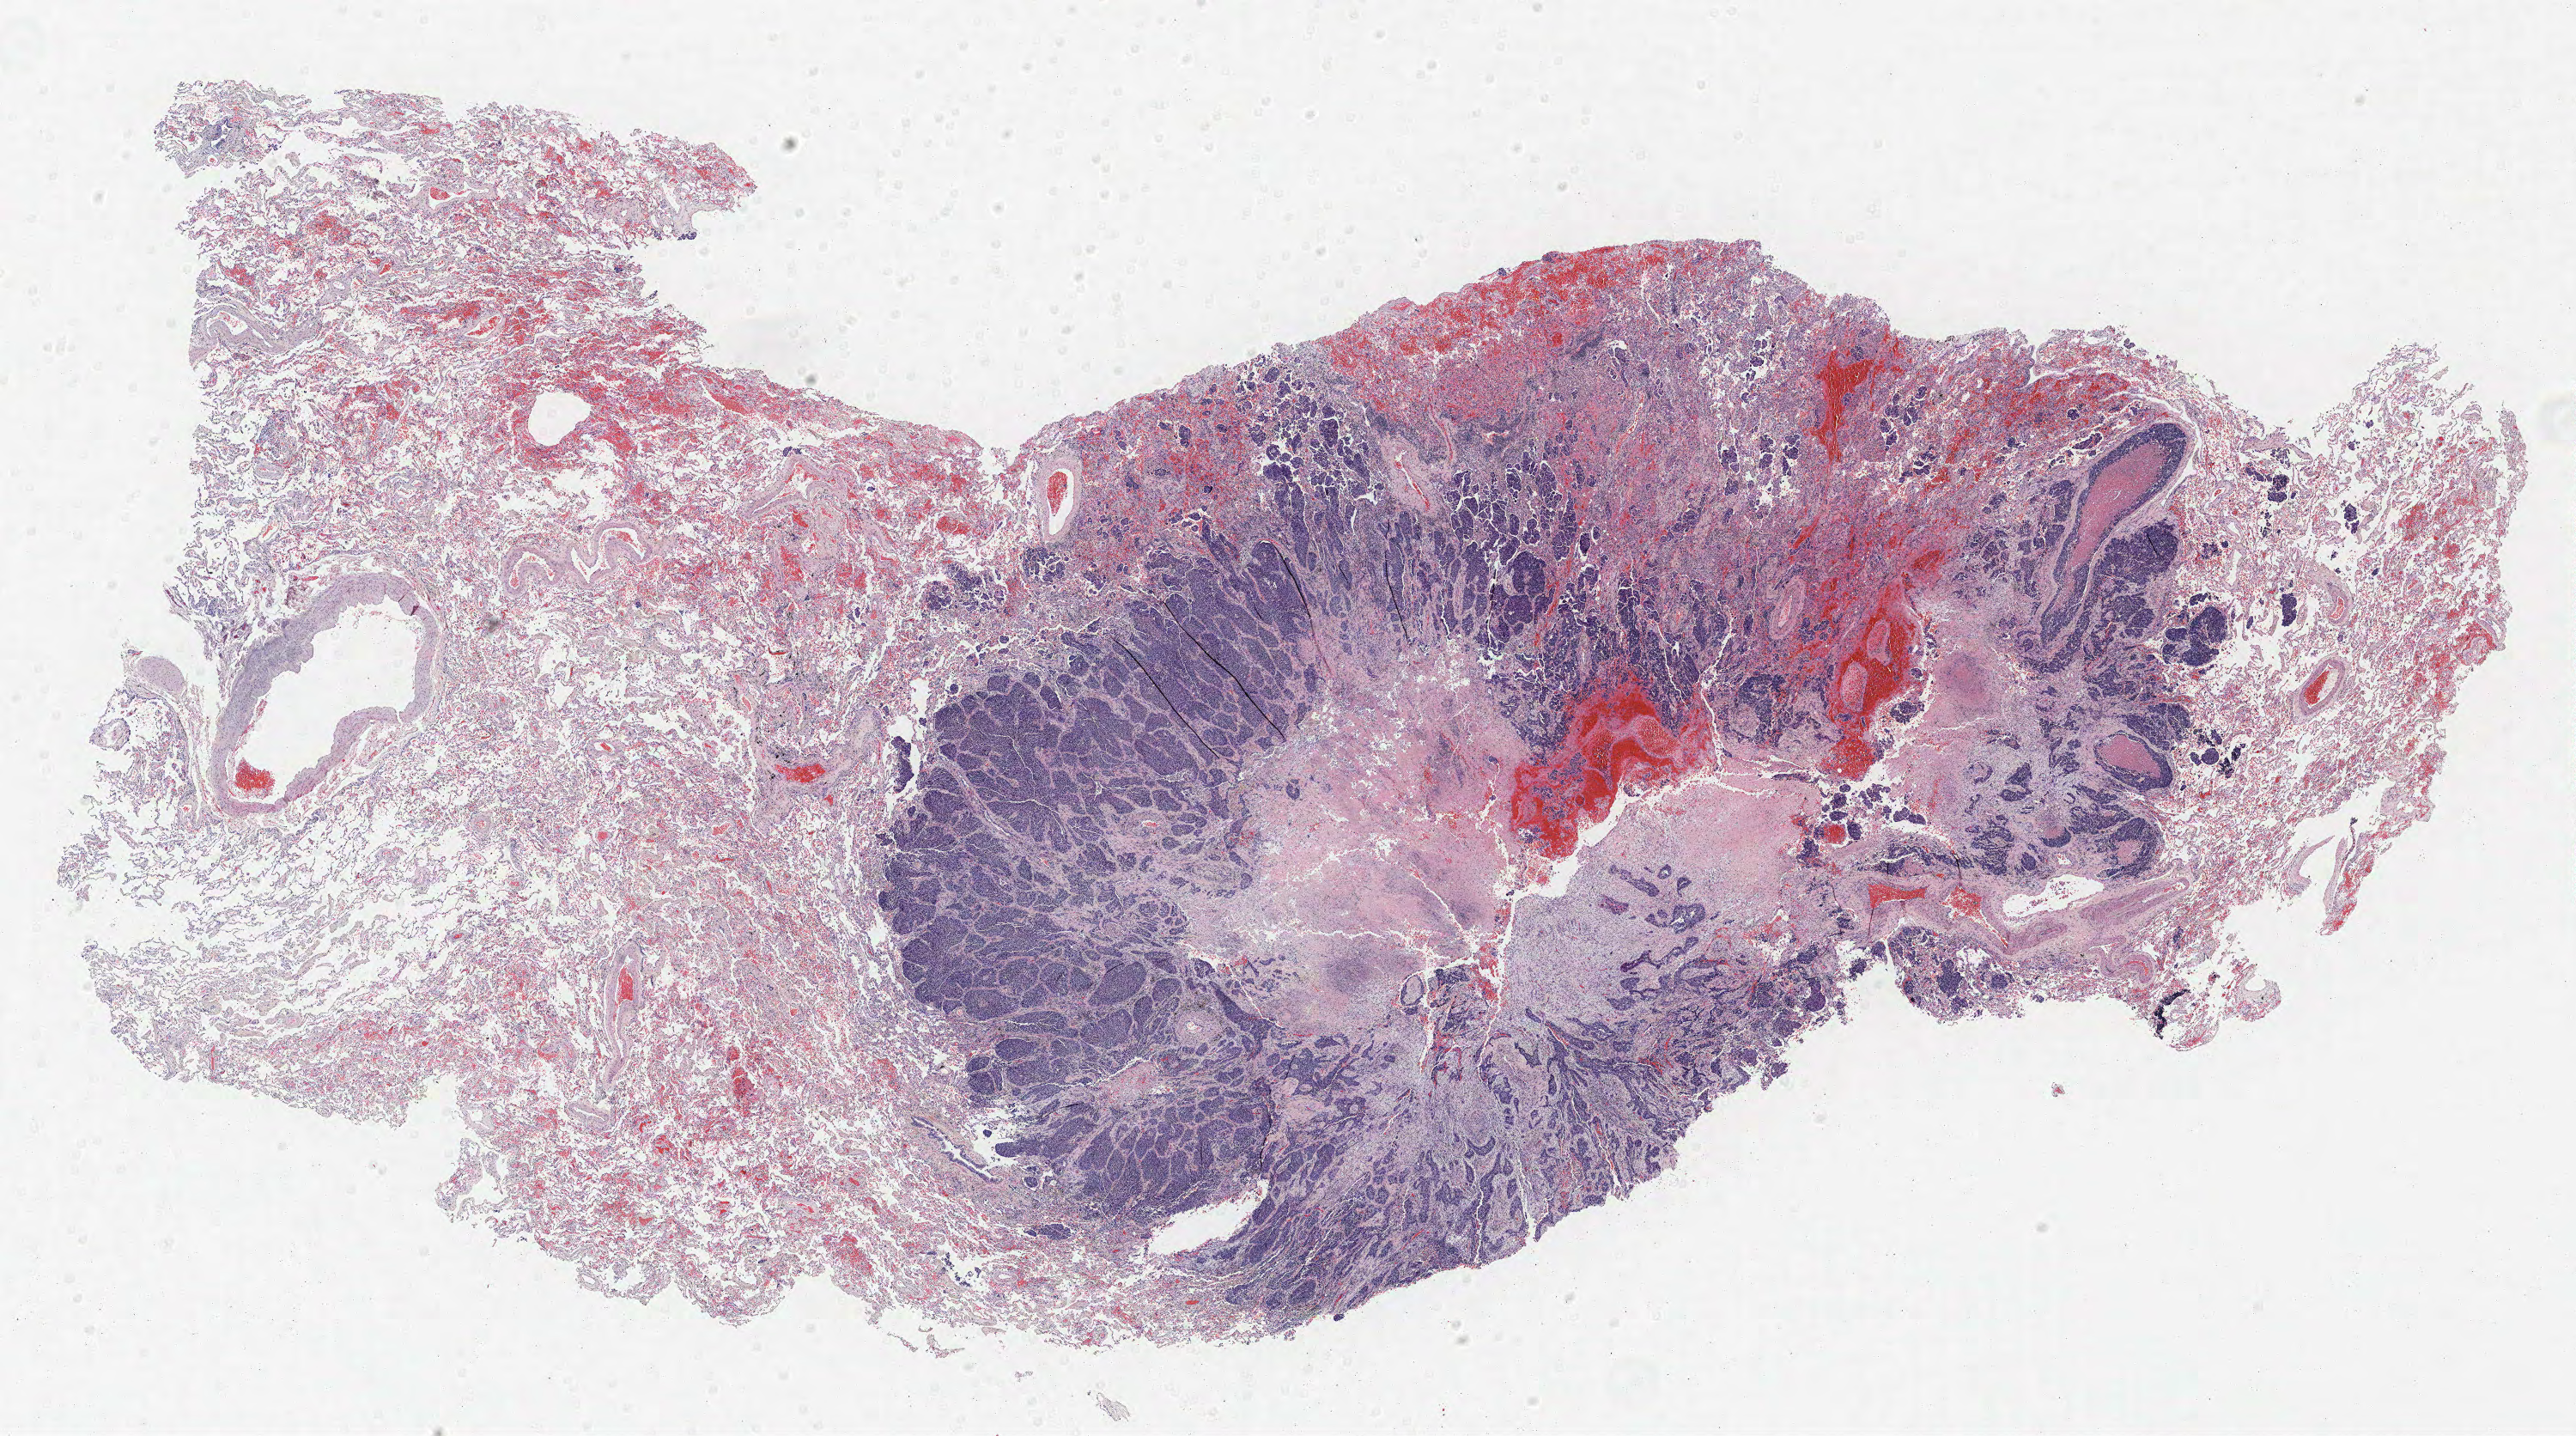
H&E whole-slide image — a low-resolution overview of the entire scanned area, about 24.0 x 13.4 mm (slide scanned at 40x), formalin-fixed paraffin-embedded (FFPE) section, lung. Male, age 72 at enrolment. Grade: moderately differentiated (G2).
Stage (AJCC 6th edition): IA. Participant's lung-cancer diagnosis: Squamous cell carcinoma, NOS. Tumour size (pathology): 20 mm. Primary tumour location (clinical record): left upper lobe.